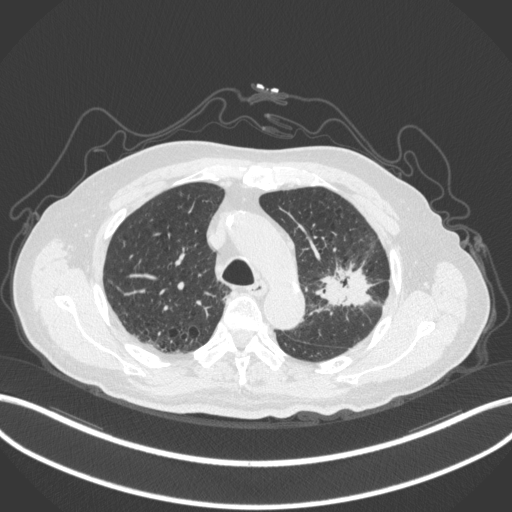
Chest CT, one axial slice; slice 214 of 331 in the series (ordered by position); lung window (W 1500 / L -600 HU); 1 mm slice thickness; 512 × 512 image matrix, field of view 400 × 400 mm. Male patient, age 79 years. From the clinical record (not read from this slice): clinical TNM (as recorded): T2a N1 M1; histopathological grade: G3.
Outlined on this slice (rectangle marked by the reading radiologist):
- lung tumour (recorded histology: adenocarcinoma): bounding box (x1, y1, x2, y2) in pixels: (308, 255, 378, 314)